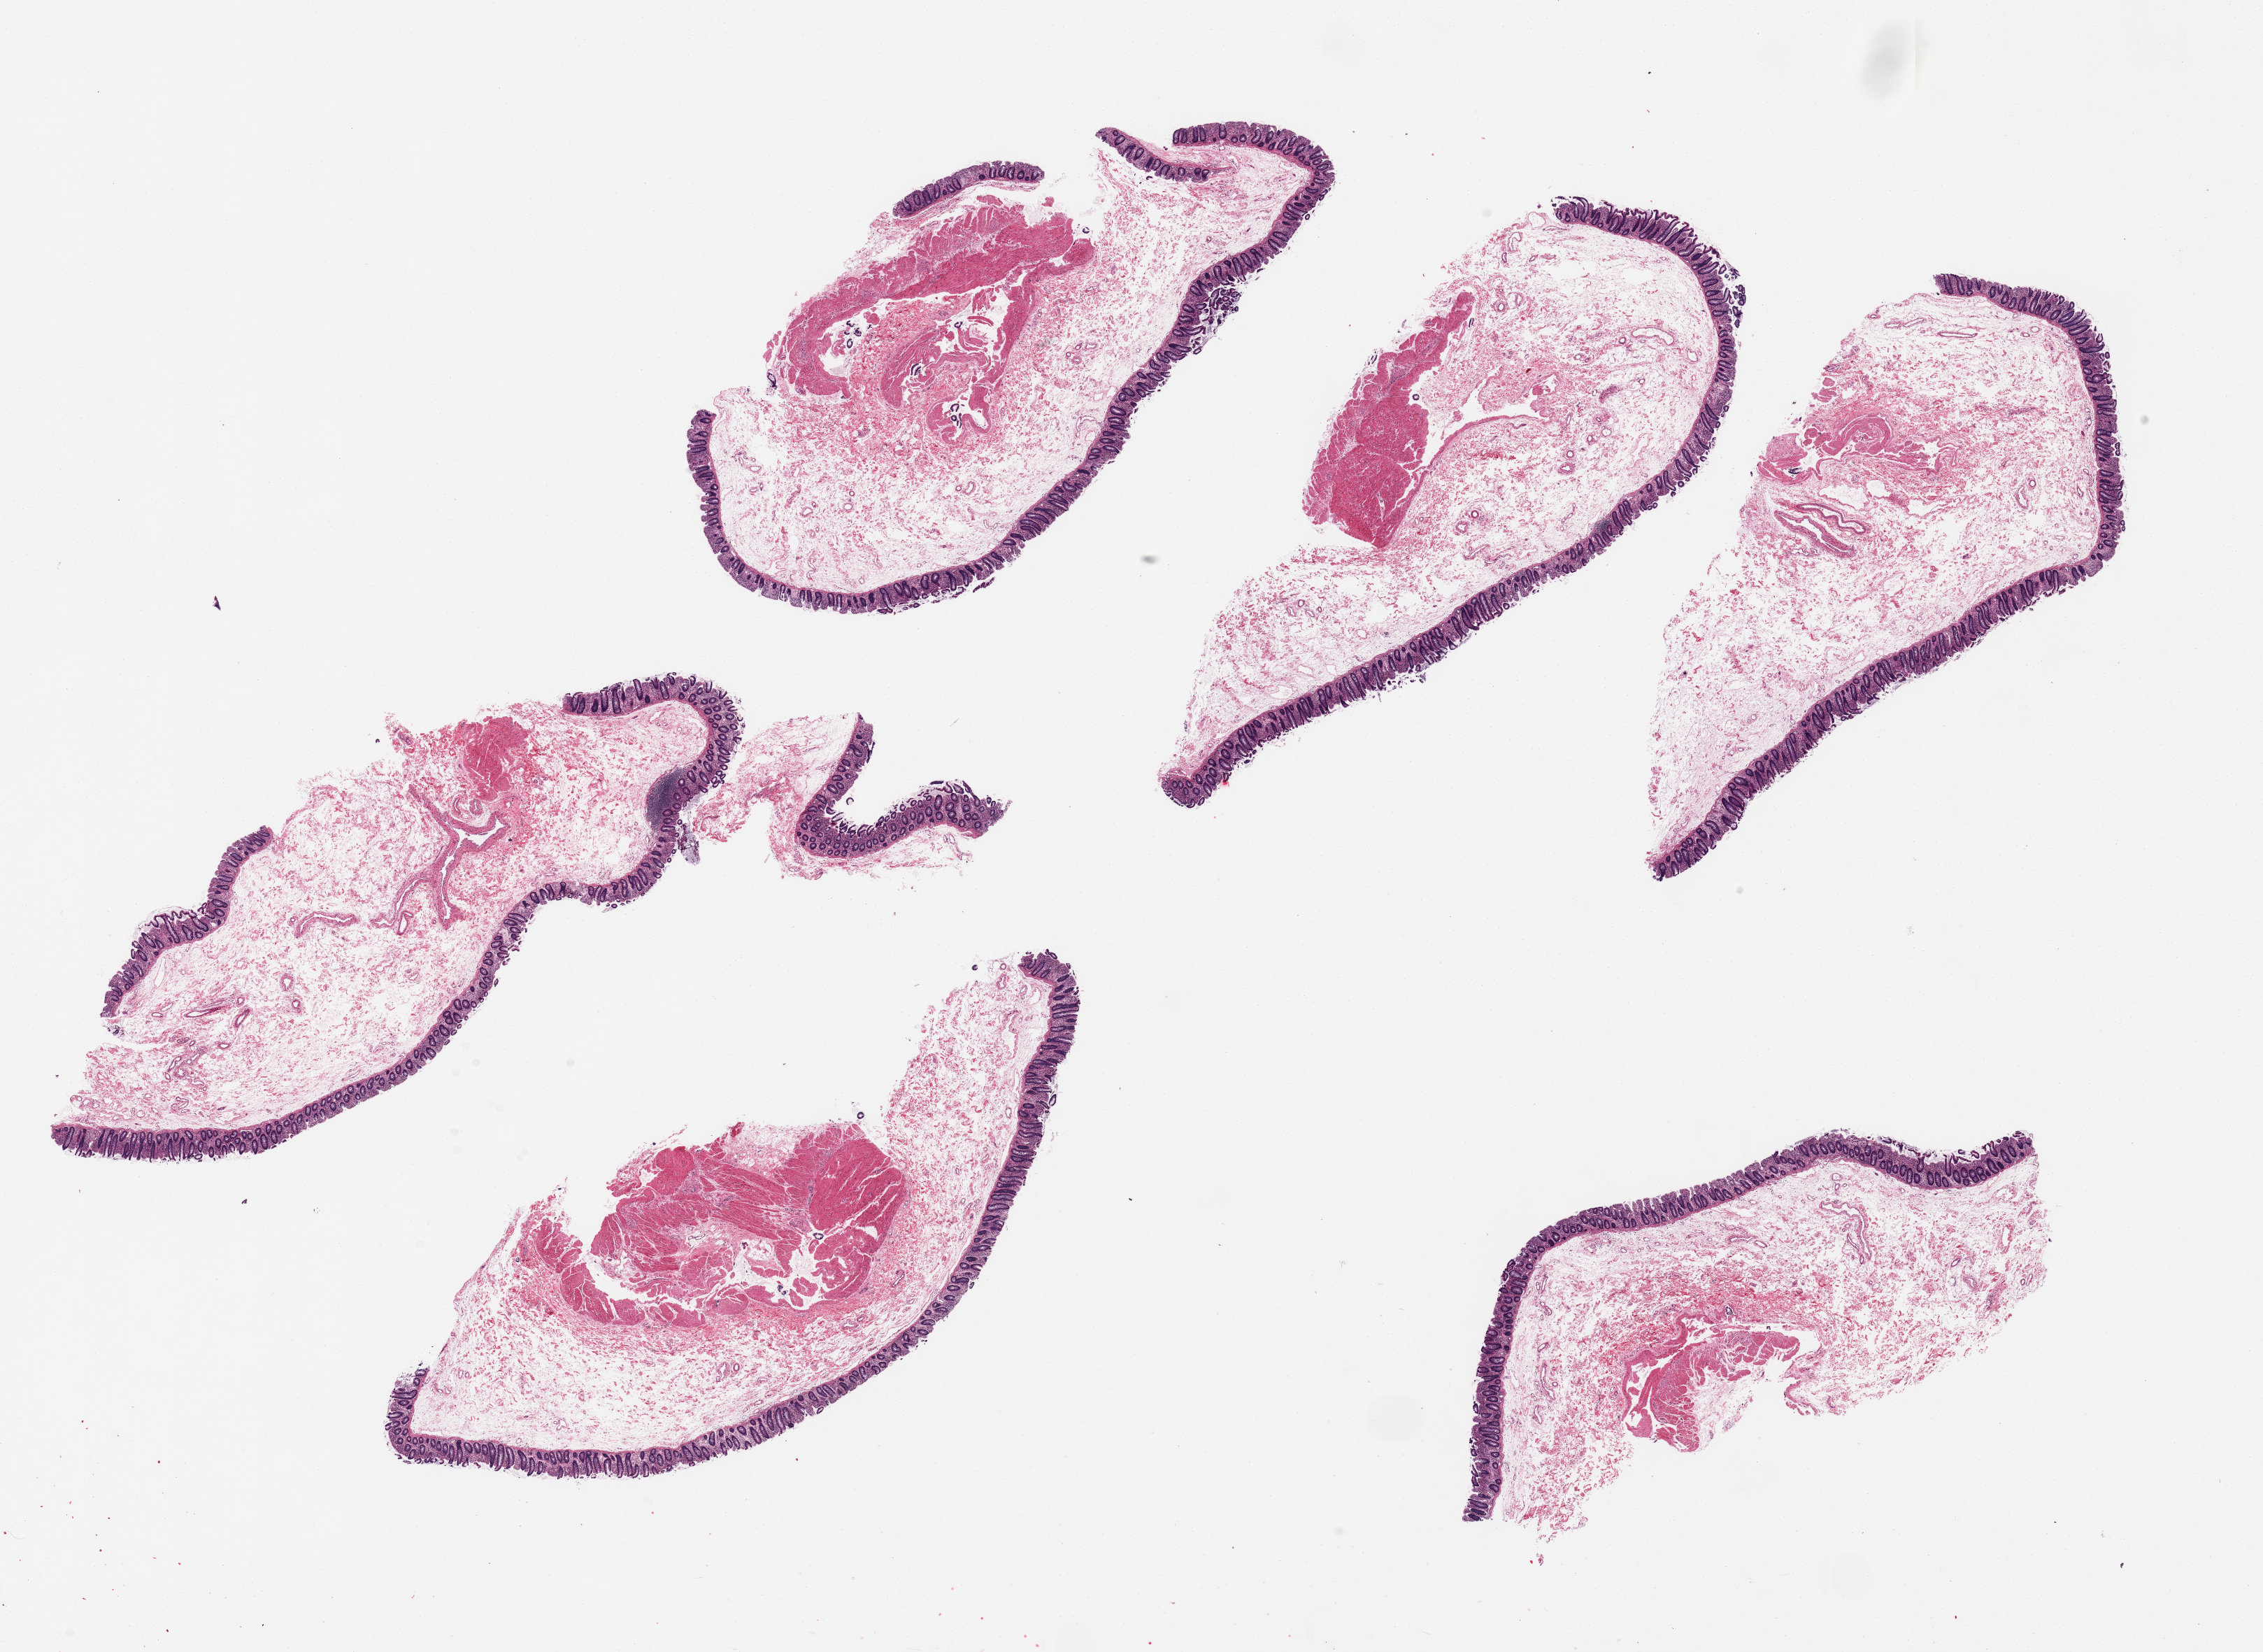
Digitized hematoxylin and eosin (H&E)-stained section, brightfield — whole scanned area (about 25.6 x 18.7 mm, acquisition: 20x scan) shown as a low-resolution overview. PAXgene-fixed, paraffin-embedded tissue. Sampled site (target tissue): transverse colon. Tissue donor sample. Female donor.
Reviewer comment on this tissue sample: 6 ~ 8x3.75mm pieces; mucosa is ~ 5-10% of thickness.